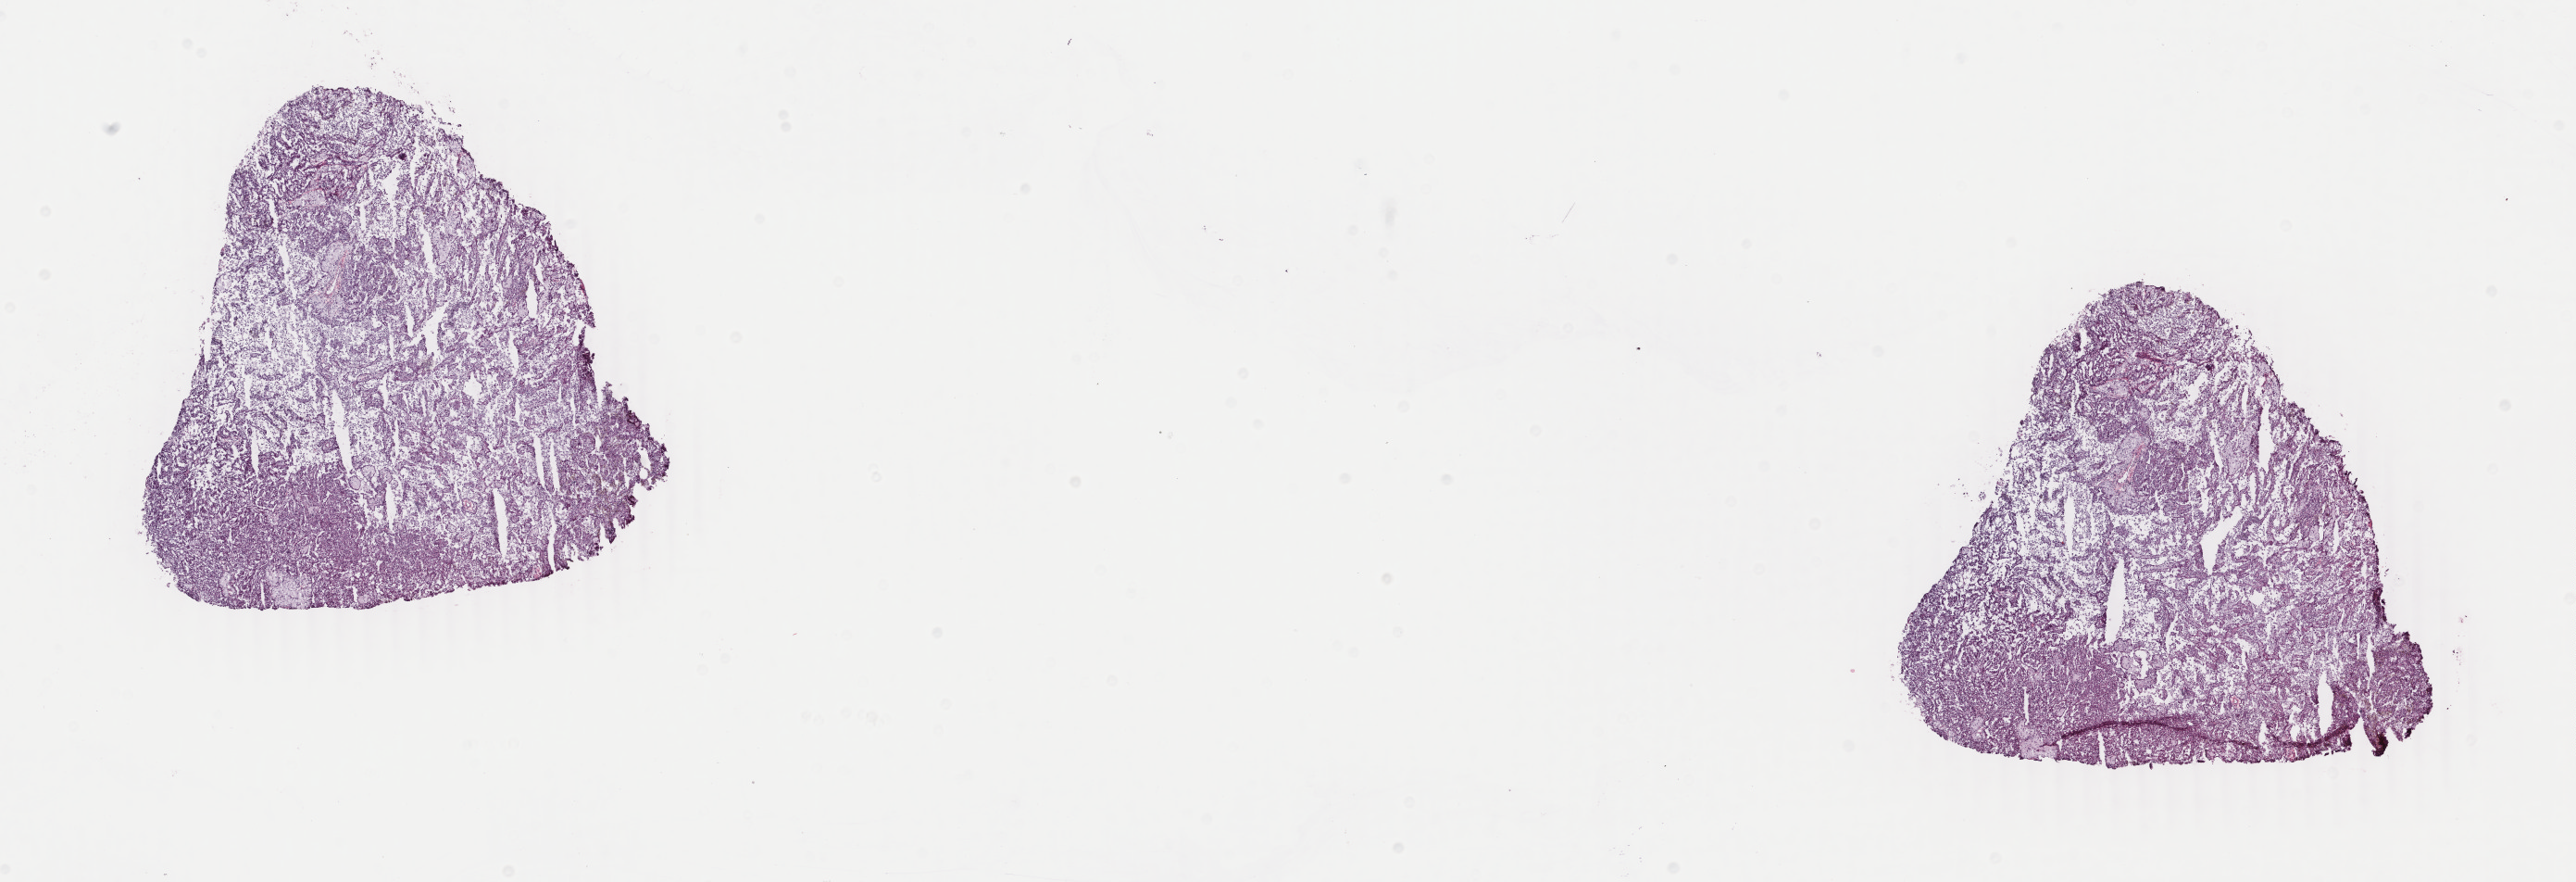
H&E whole-slide image, whole scanned area (about 22.1 x 7.6 mm, from a 40x scan) shown as a low-resolution overview, frozen section from the top of the tissue portion, sample: primary tumour, kidney. Patient: male, age at initial diagnosis 50 years. Pathologist review of this section (percent, as recorded): tumour cells 100%, tumour nuclei 80%, normal cells 0%, stromal cells 0%, necrosis 0%. Infiltration values recorded for this section: lymphocyte infiltration 2%, monocyte infiltration 0%, neutrophil infiltration 0%.
- TNM: T2b NX M0
- AJCC pathologic stage: II
- diagnosis: Papillary adenocarcinoma, NOS
- laterality: right